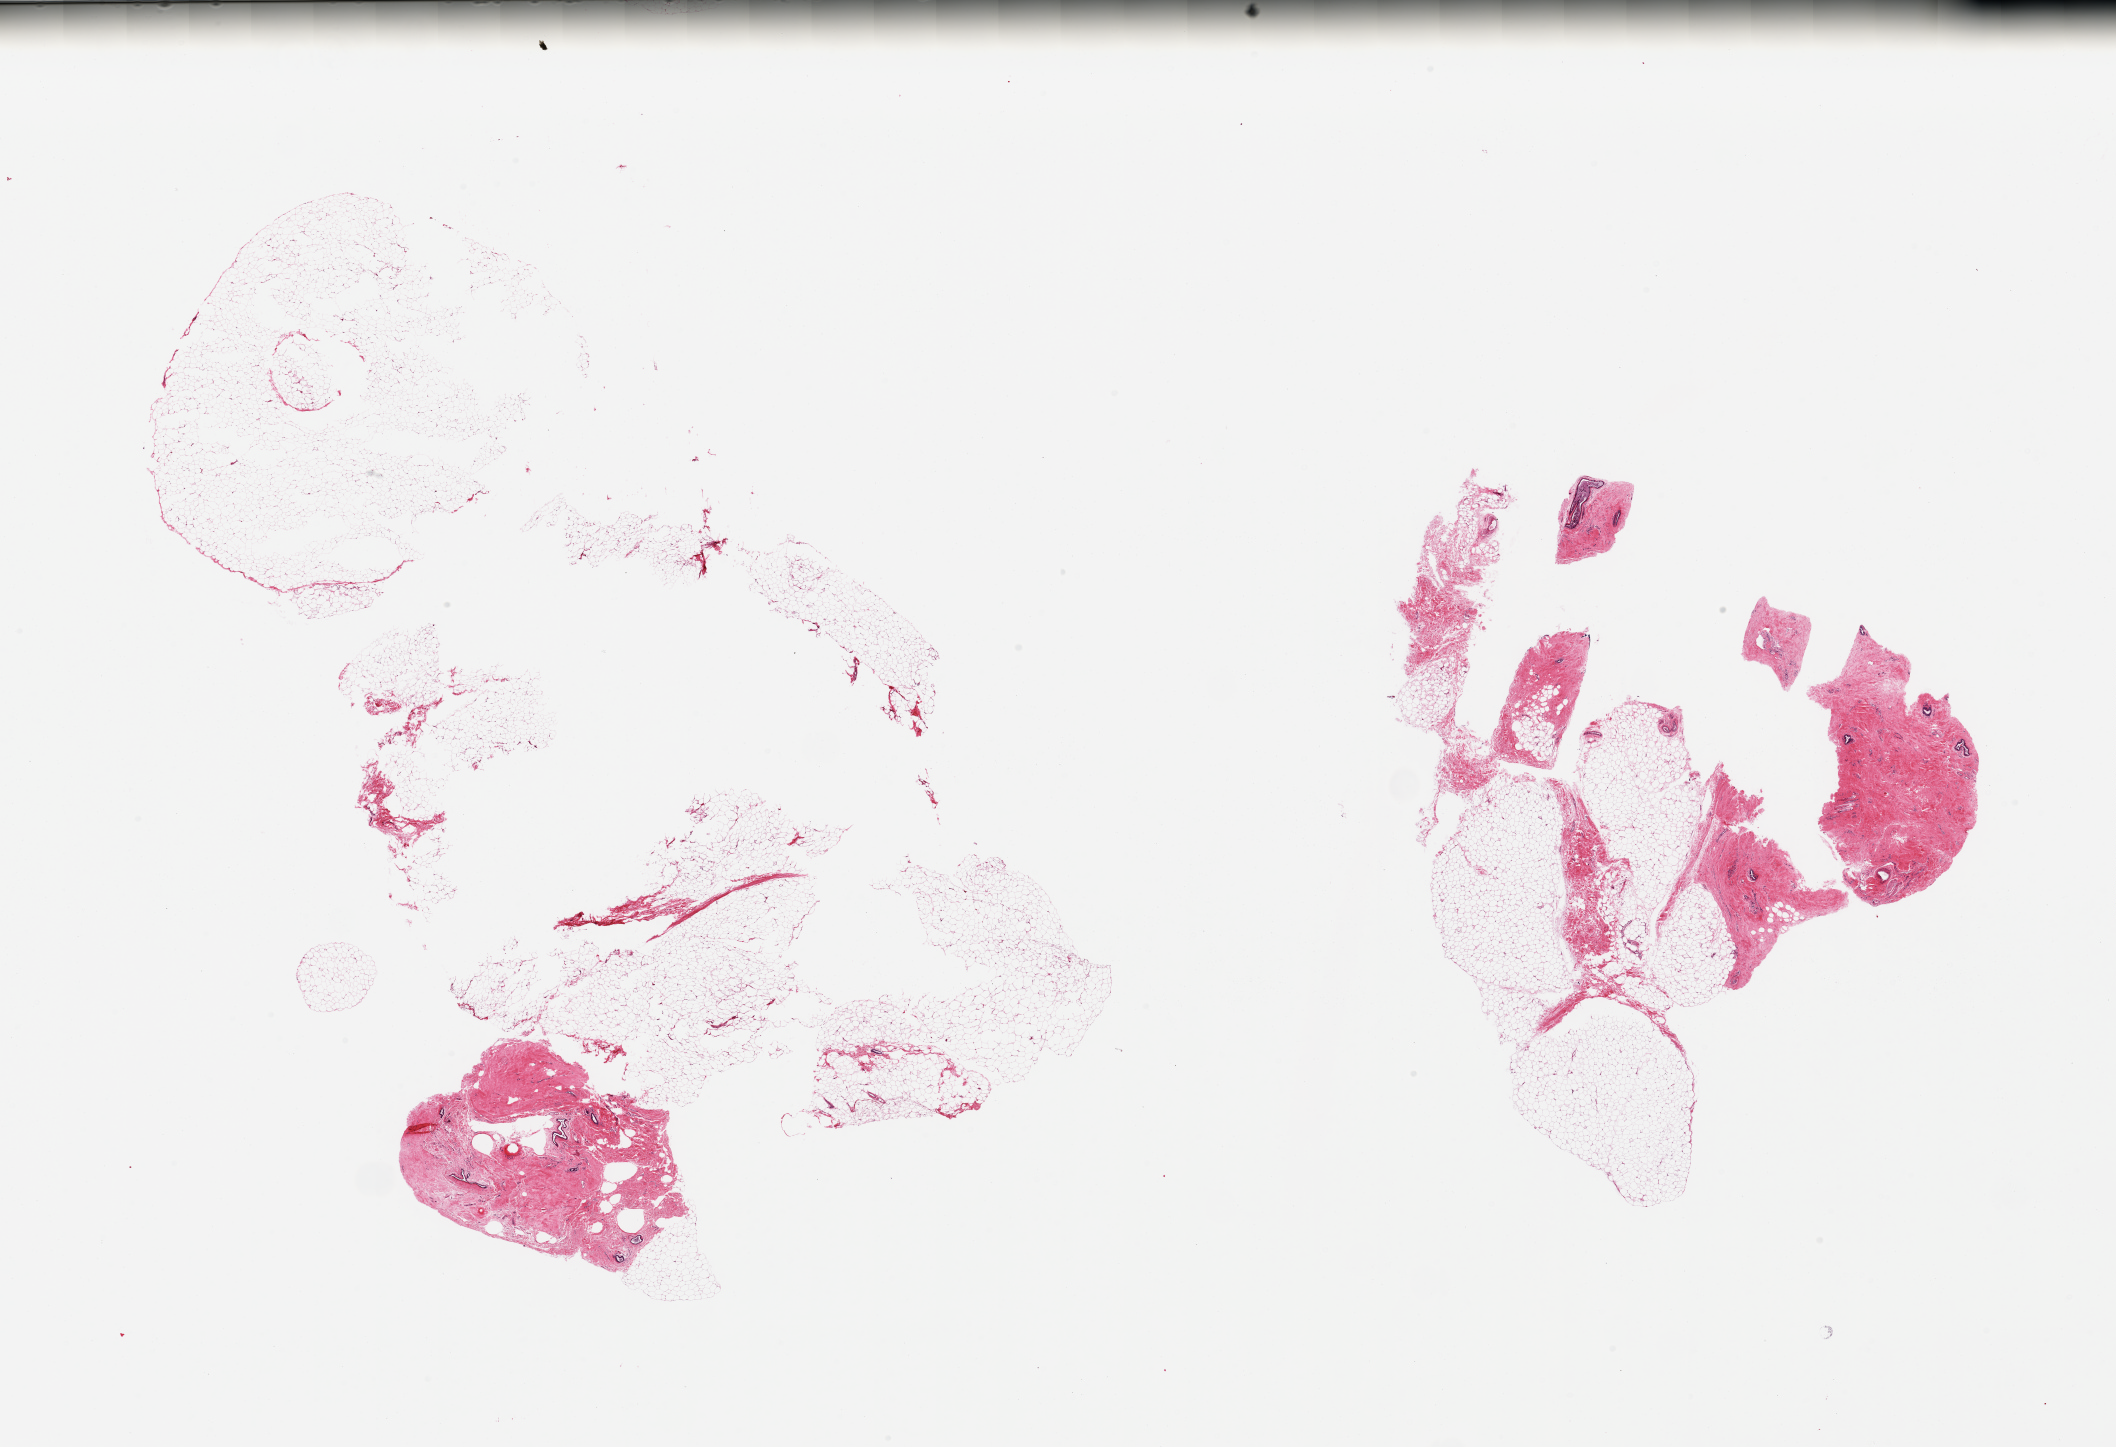
H&E whole-slide image, brightfield, whole scanned area (about 33.5 x 22.9 mm) shown as a low-resolution overview, PAXgene-fixed paraffin-embedded (PFPE) section, section of breast (target tissue), donor tissue sample. Donor: male.
* reviewer comment on this tissue sample: 2 pieces, gynecomastoid stromal and ductal (rep) hyperplasia